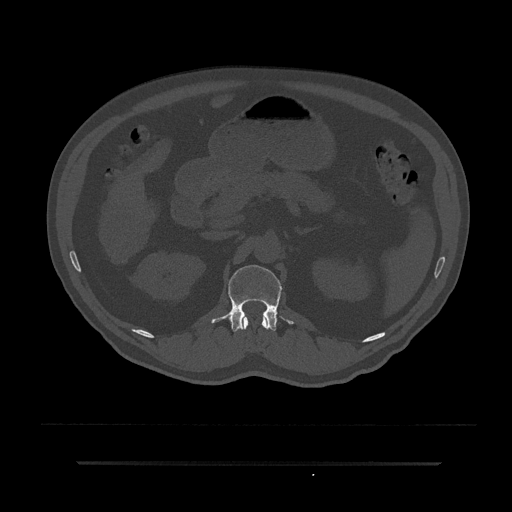
CT including the spine, one axial slice. Slice 164 of 797 in the series (ordered by position). 120 kVp. Bone window (W 1800 / L 400 HU). 0.5 mm slice thickness. 512 × 512 image matrix, field of view 464 × 464 mm. Male patient, age 59 years. From the clinical record (not read from this slice): primary cancer: bile ducts.
Annotated regions visible in this slice (semi-automatically segmented with operator editing):
- L1 vertebra: bounding box [x1, y1, x2, y2] px = [211, 265, 294, 332]
- T12 vertebra: [240, 316, 268, 330]